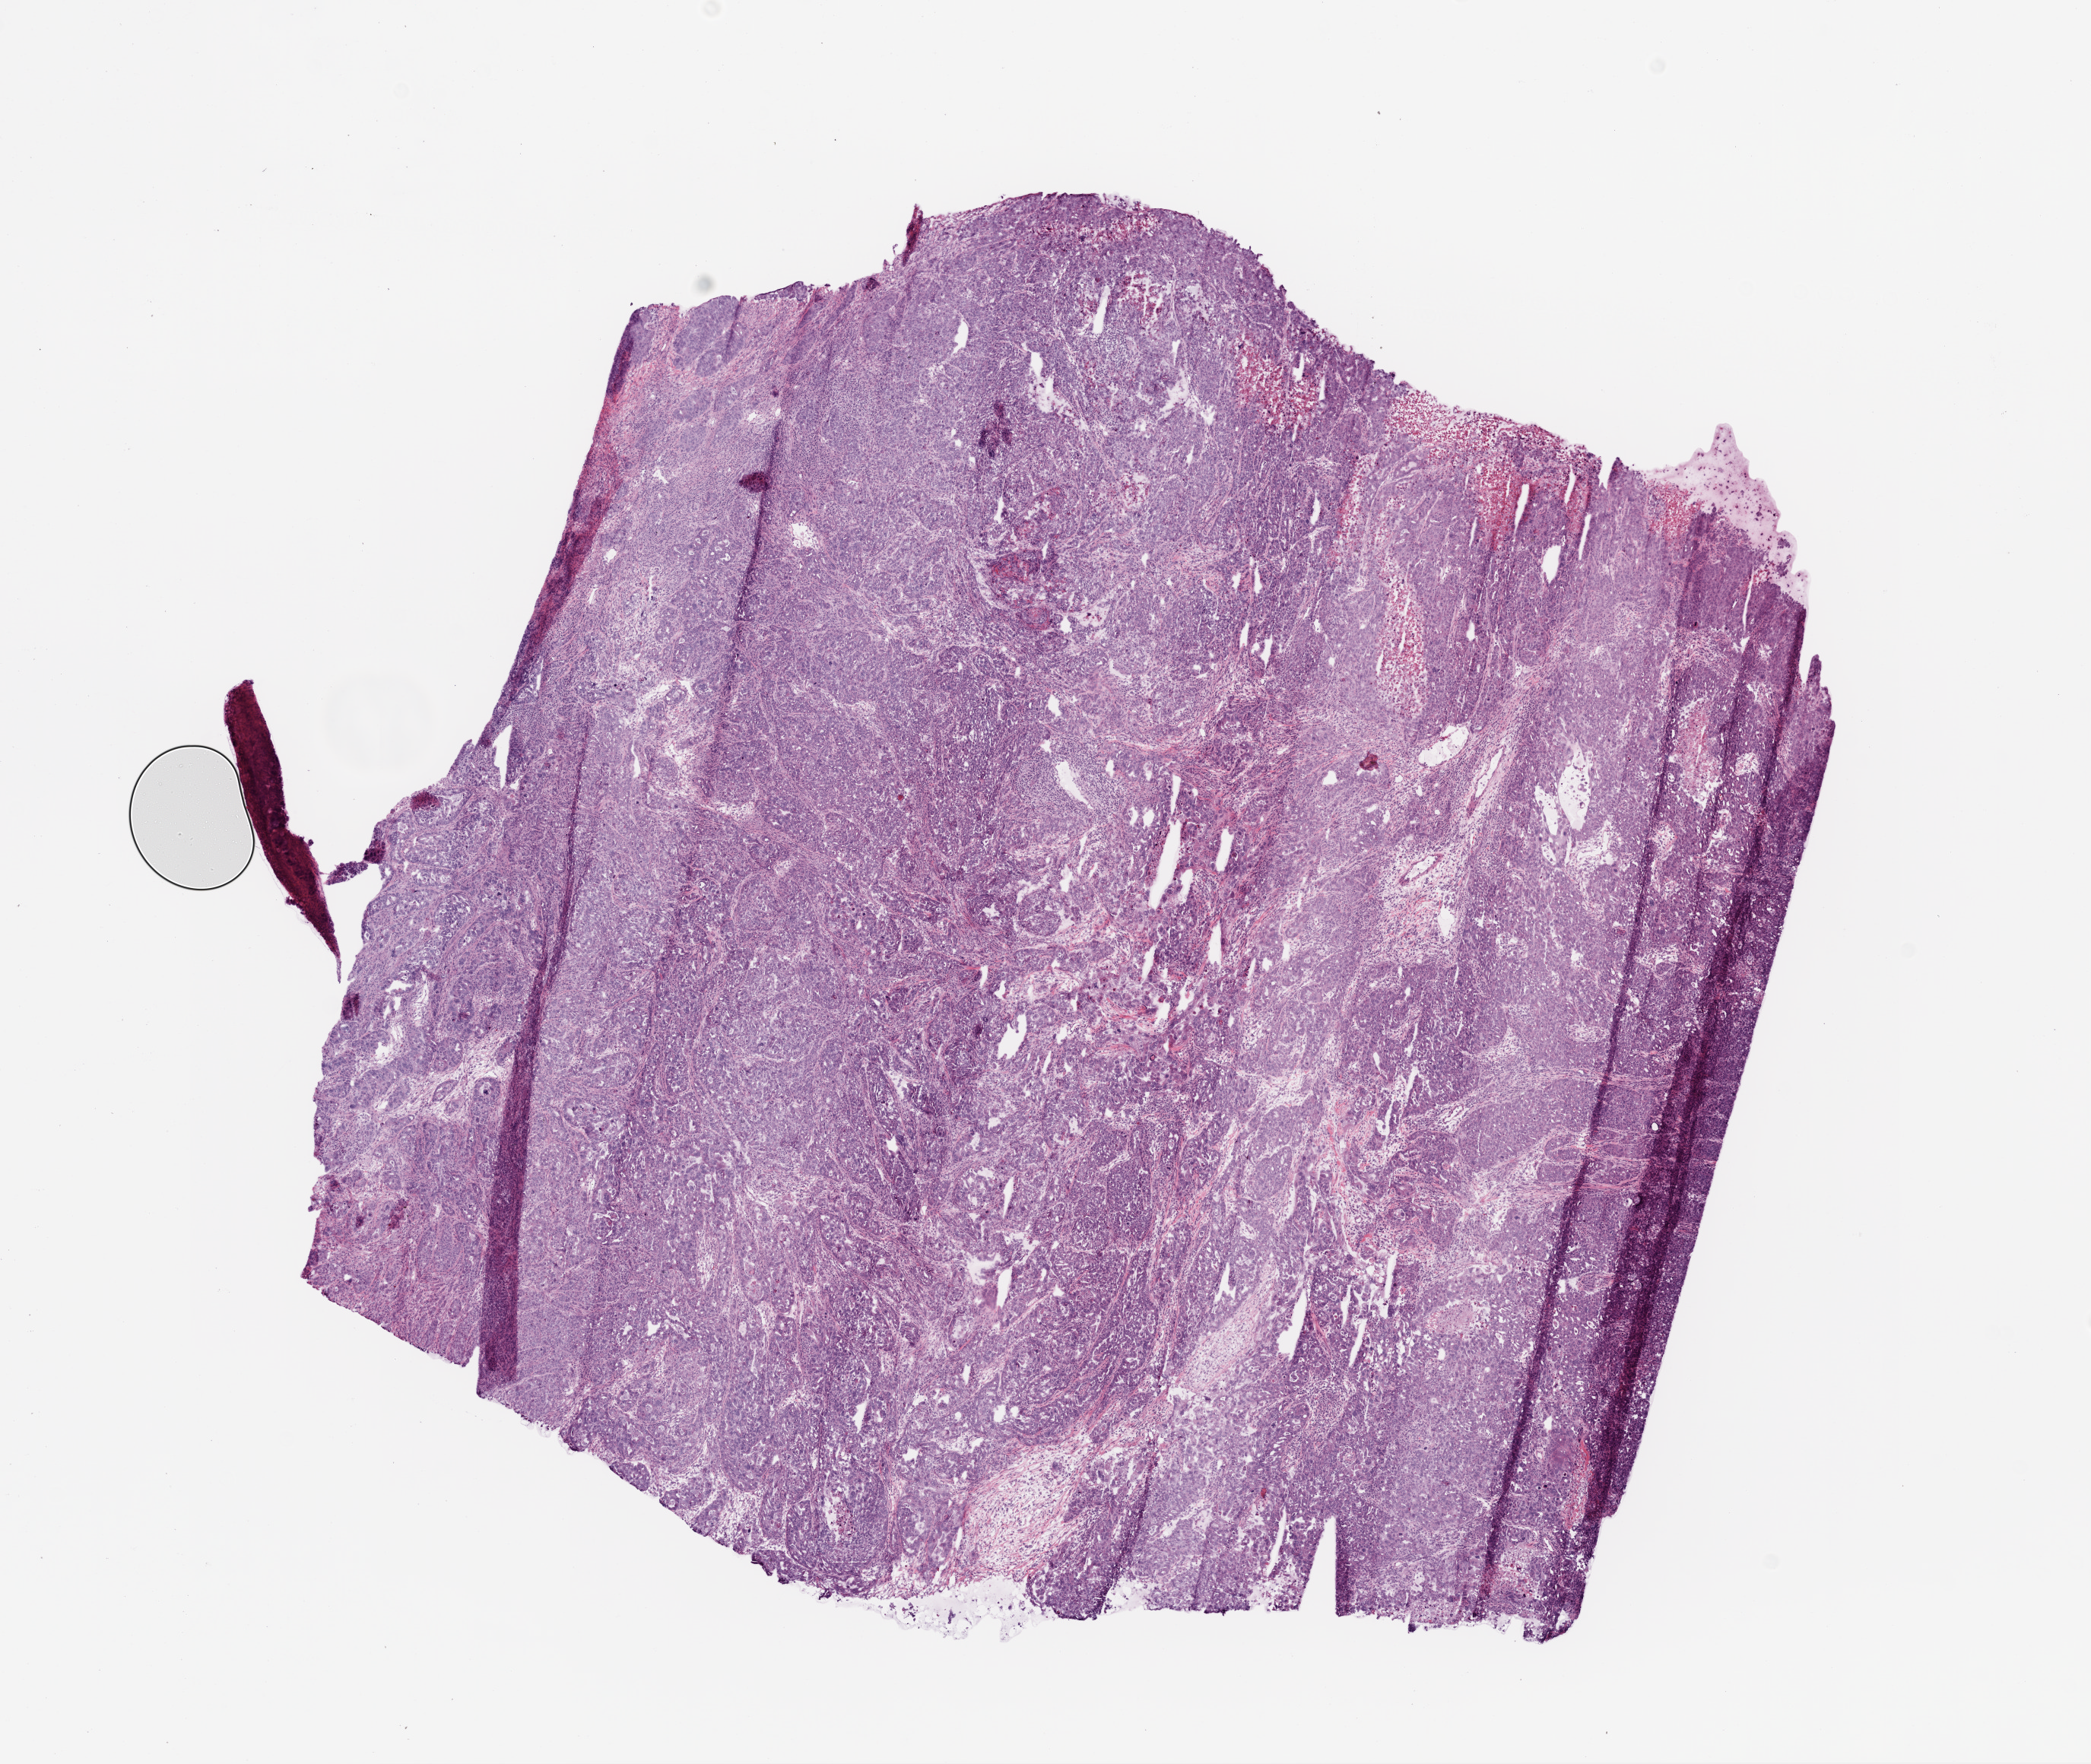
Whole-slide histology image, Hematoxylin and eosin (H&E) stained — low-resolution overview of the scanned area, about 11.0 x 9.3 mm (from a 20x scan); frozen section; ovary, primary tumour sample. Female patient; age at initial diagnosis 63 years. Histologic grade: G3 (poorly differentiated). Composition of this section per pathologist review: tumour cells 93%, tumour nuclei 95%, normal cells 0%, stromal cells 2%, necrosis 5%.
* FIGO stage: IIC
* diagnosis: Serous cystadenocarcinoma, NOS